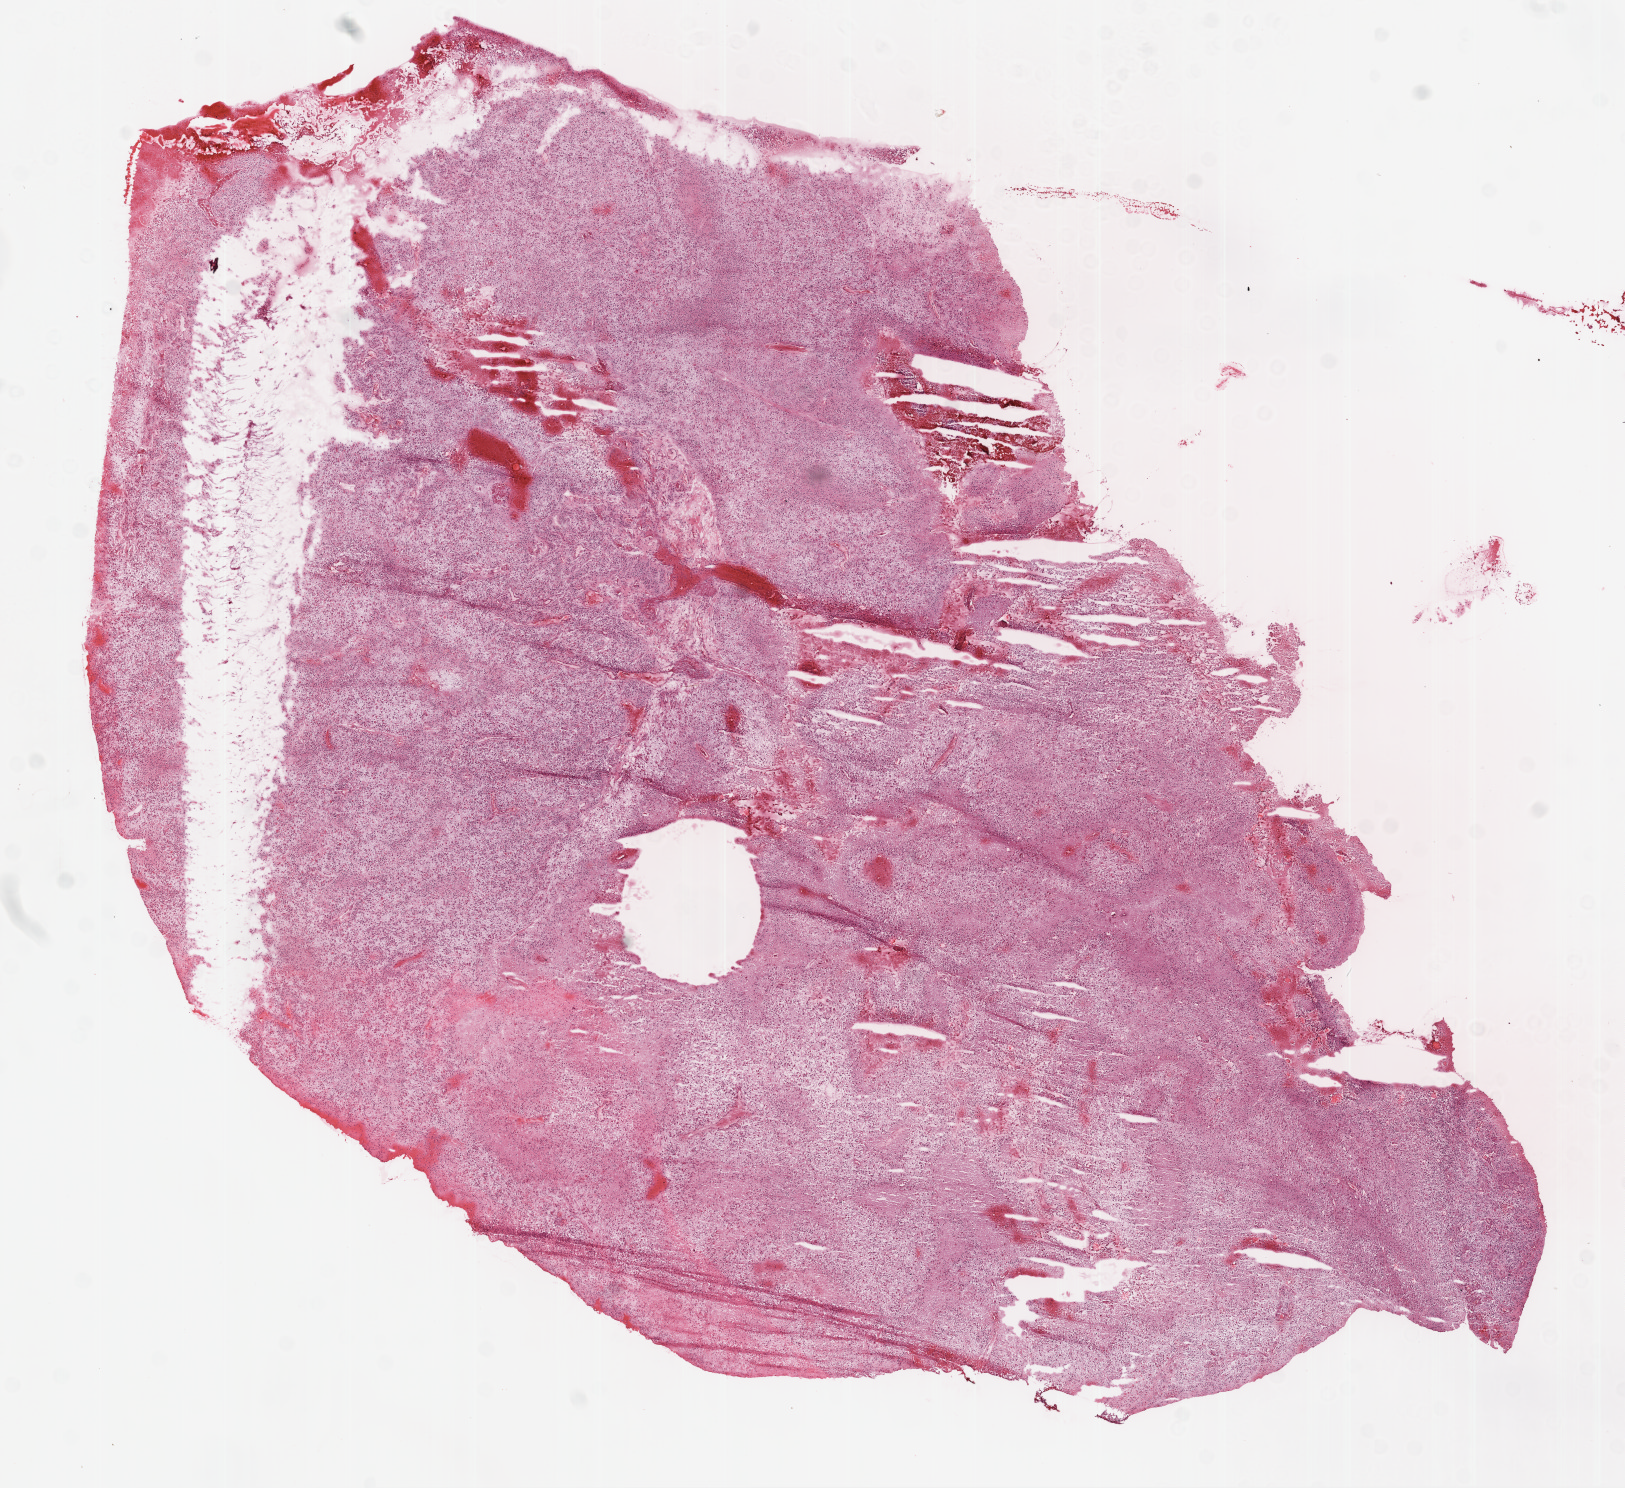
Digitized H&E-stained tissue section (whole slide) — a low-resolution overview of the entire scanned area, about 13.0 x 11.9 mm. Frozen section. Brain, primary tumour sample. Male patient; age at initial diagnosis 59 years. Composition of this section per pathologist review: tumour cells 90%, tumour nuclei 80%, normal cells 0%, stromal cells 0%, necrosis 10%.
Pathologic diagnosis: Glioblastoma.